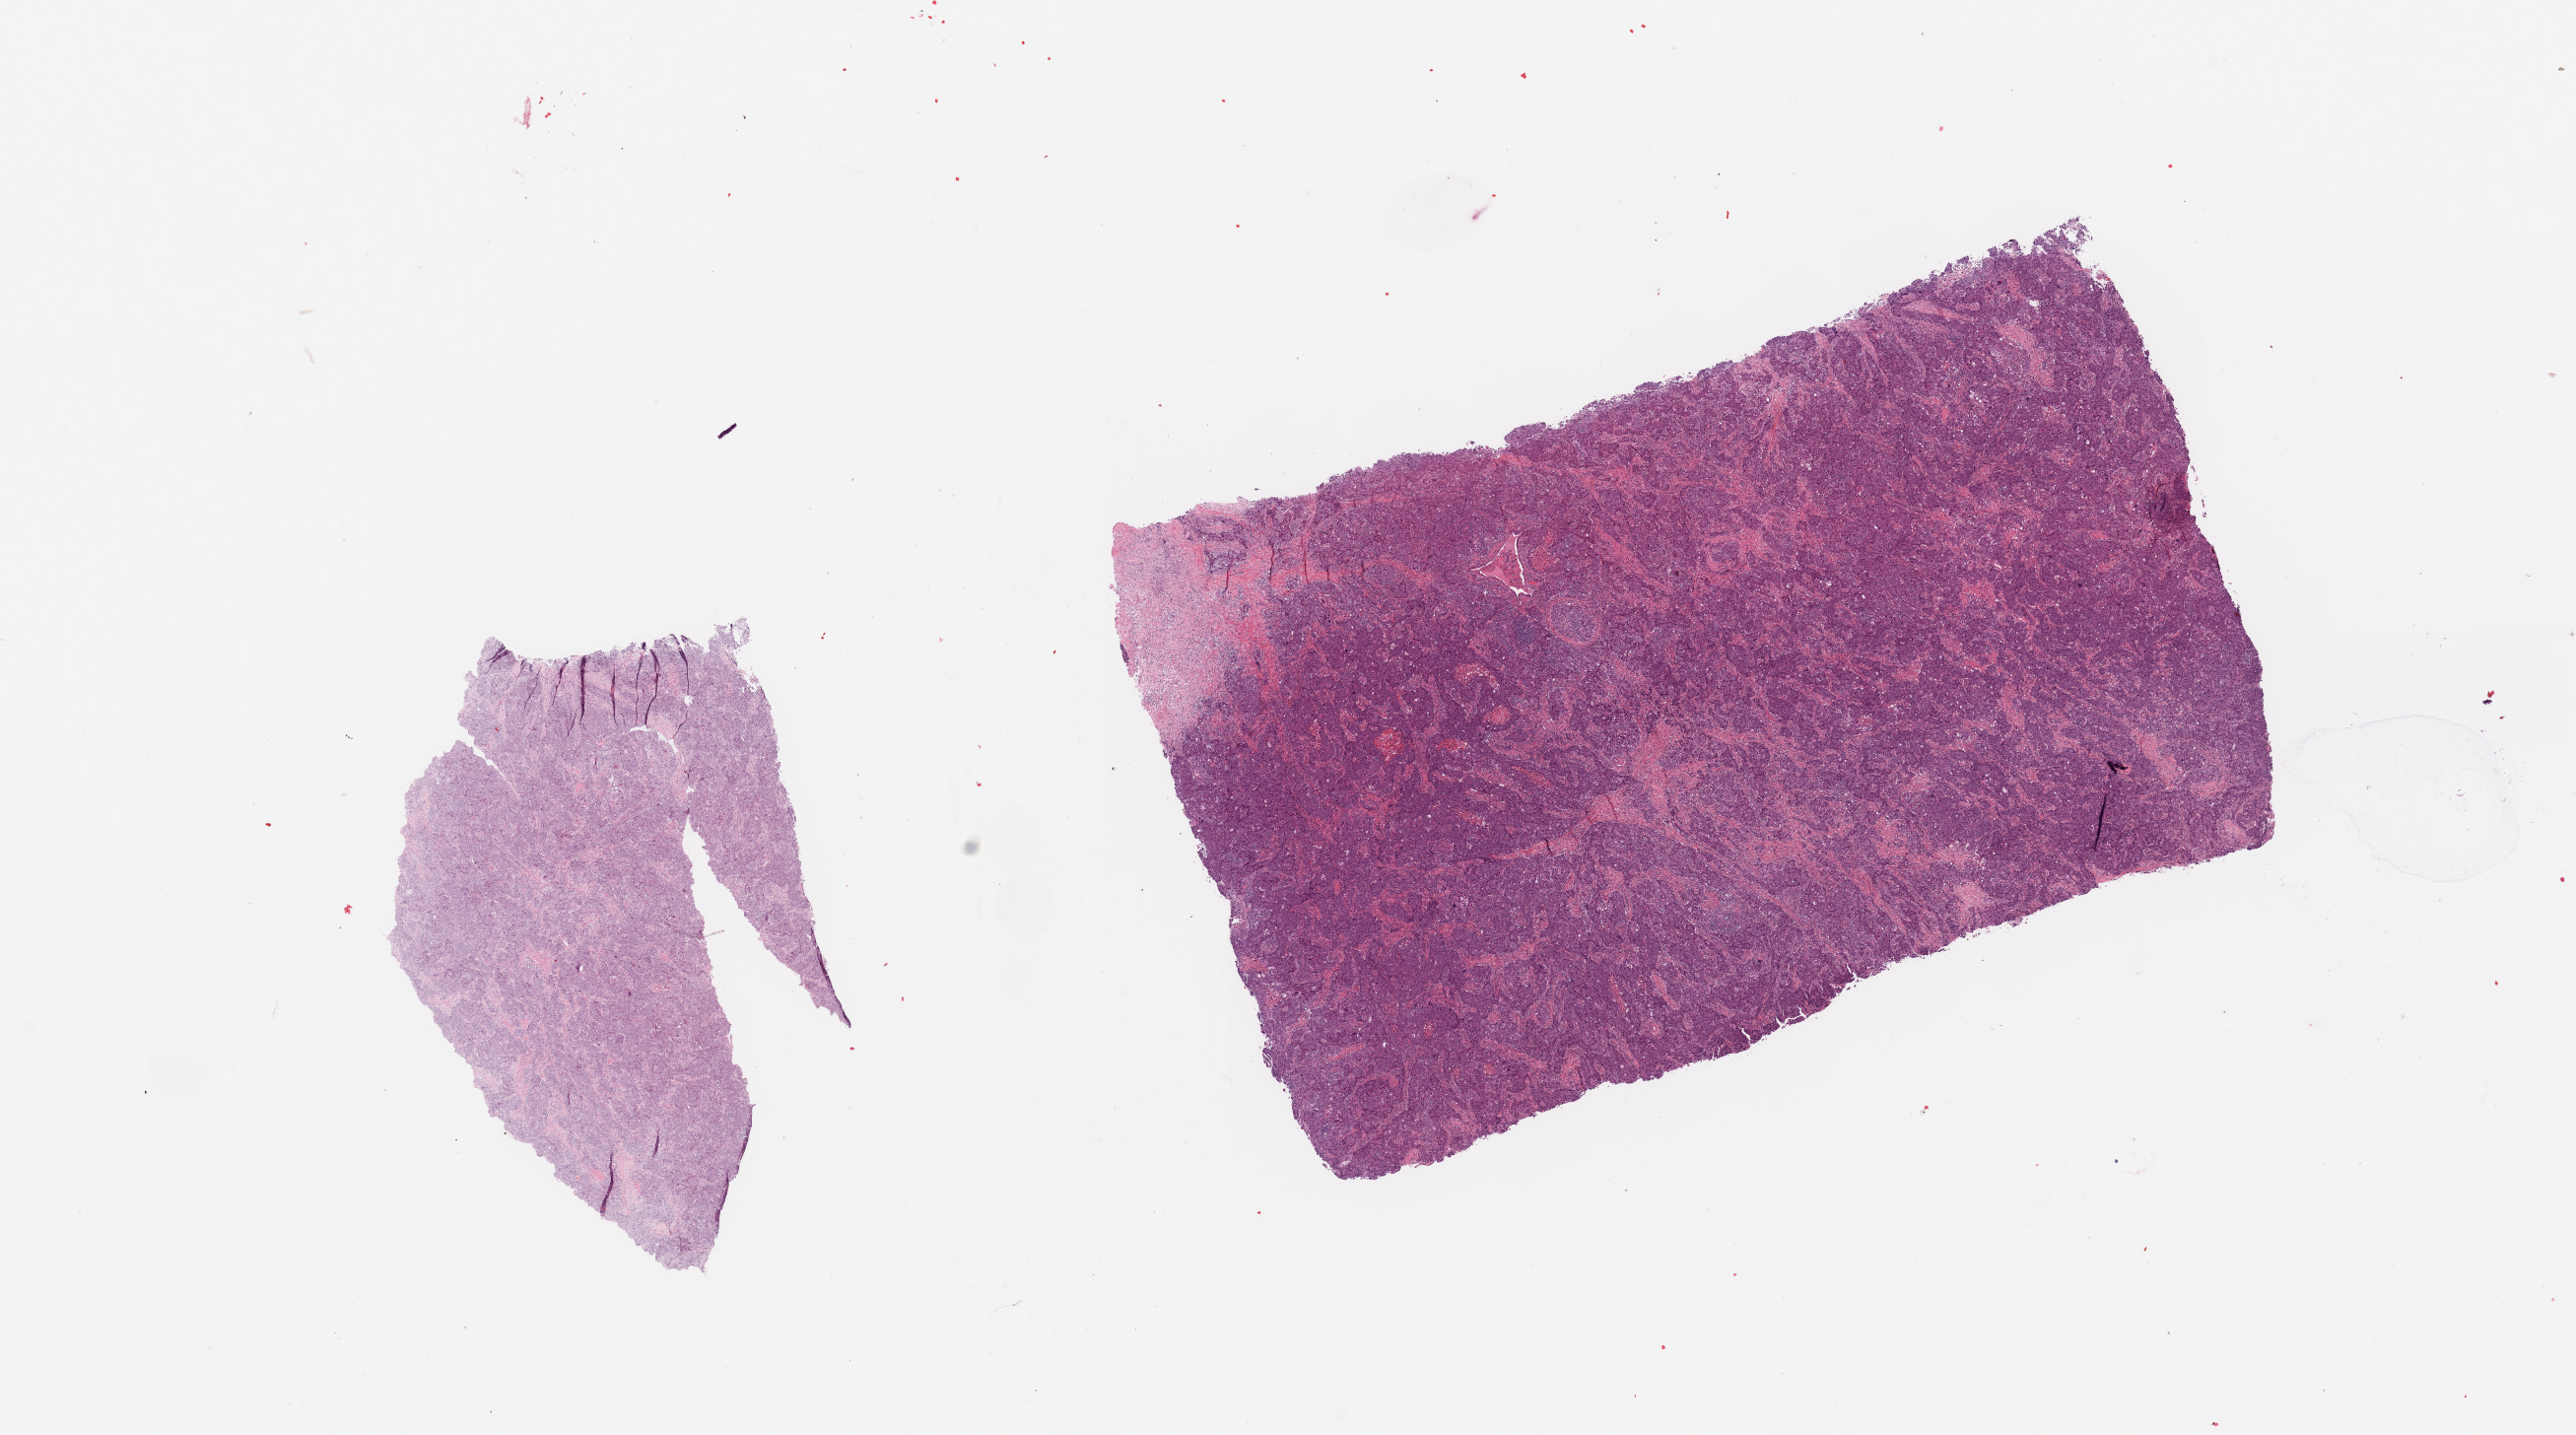
Whole-slide histology image, H&E, a low-resolution overview of the entire scanned area, about 20.7 x 11.5 mm (from a 20x scan), tumour tissue sample, sampled site: lung. Male, 67 y/o. Histologic grade: G3 (poorly differentiated). Composition of this section per pathologist review: tumour nuclei 80%, necrosis 5%.
Primary tumour site (as recorded): right lower lobe. Histologic diagnosis: Adenocarcinoma, NOS. AJCC pathologic stage: IIA.